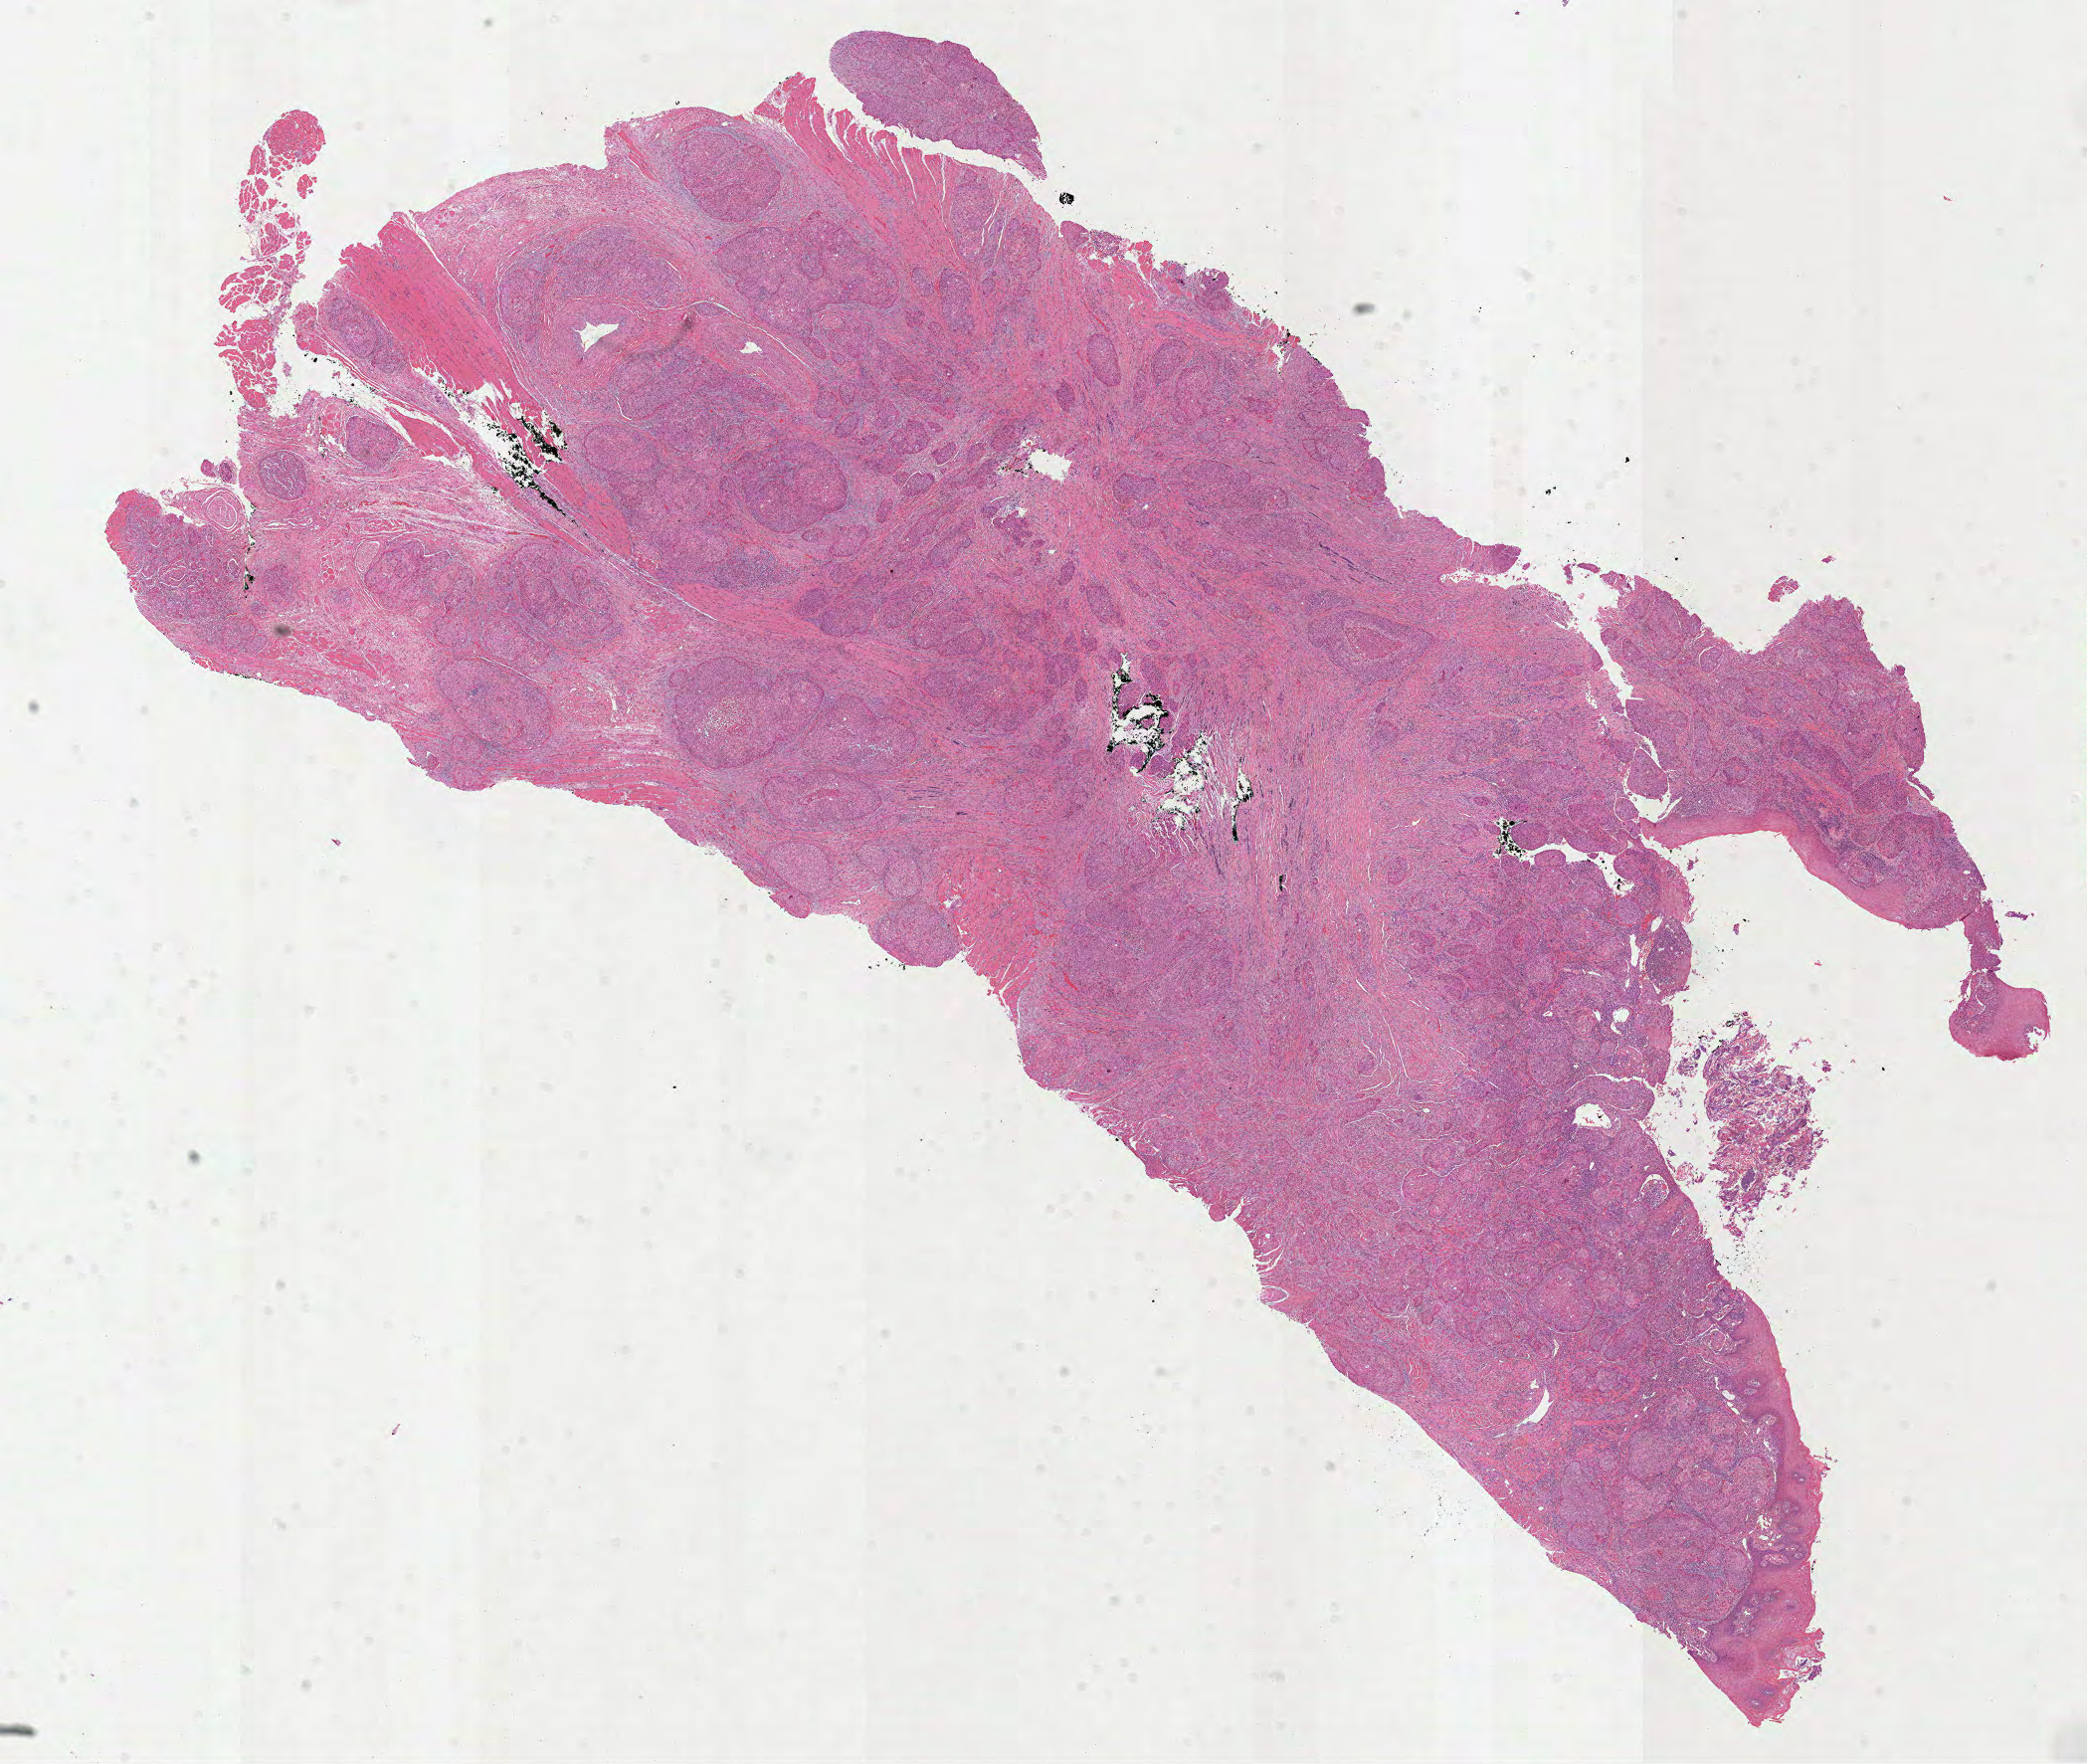
Whole-slide histology image, H&E — shown as a low-resolution overview of the whole scanned area (about 16.9 x 14.3 mm); formalin-fixed paraffin-embedded (FFPE) diagnostic section; head and neck, primary tumour sample. Male patient; age at initial diagnosis 63 years. Histologic grade: G3 (poorly differentiated).
AJCC pathologic stage: IVA (7th edition). Pathologic diagnosis: Squamous cell carcinoma, NOS (base of tongue, NOS). TNM: T3 N2c M0.